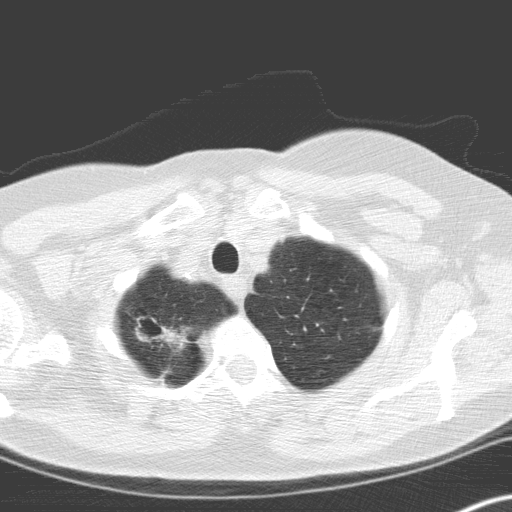
Axial slice from a low-dose chest CT screening exam, second annual screen, lung window (W 1500 / L -600 HU), standard (soft-tissue) reconstruction kernel (C), slice 25 of 166 in the series, 512 × 512 image matrix, field of view 306 × 306 mm. Female, age 60 years at enrolment. Current smoker at enrolment.
Lesion marked by an expert reader, bounding box [x1, y1, x2, y2] px = [128, 307, 206, 376]. The exam's reader record, not a measurement of the box and not confirmed to be the same lesion: non-calcified nodule or mass ≥4 mm, right upper lobe, 12 × 8 mm, spiculated (stellate) margins, soft tissue attenuation, pre-existing on the prior screen: no. Lung cancer was diagnosed 58 days after this screen: squamous cell carcinoma, keratinizing, NOS, right upper lobe, moderately differentiated (G2), stage IA (AJCC 6th edition), 20 mm at pathology.